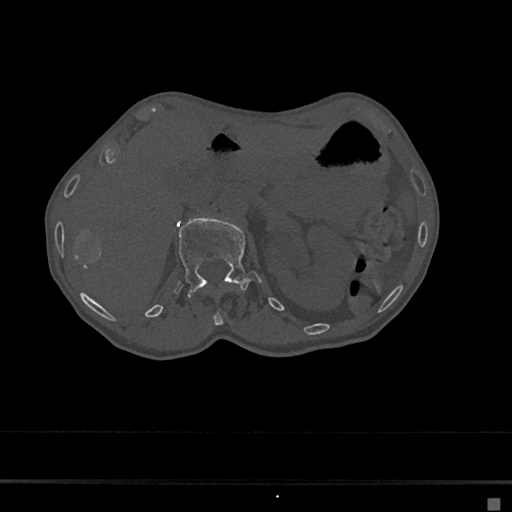
CT including the spine, one axial slice; position 78 of 797 along the scan axis; reconstruction kernel Br40s/3; 120 kVp; bone window (W 1800 / L 400 HU); 512 × 512 image matrix, field of view 360 × 360 mm. Patient: female, 68 years. From the clinical record (not read from this slice): primary cancer: renal.
Annotated regions visible in this slice (semi-automatic segmentation, software-assisted and operator-edited):
- L1 vertebra: box from (x=175, y=216) to (x=261, y=296) px
- T12 vertebra: (x=212, y=289)–(x=235, y=326)